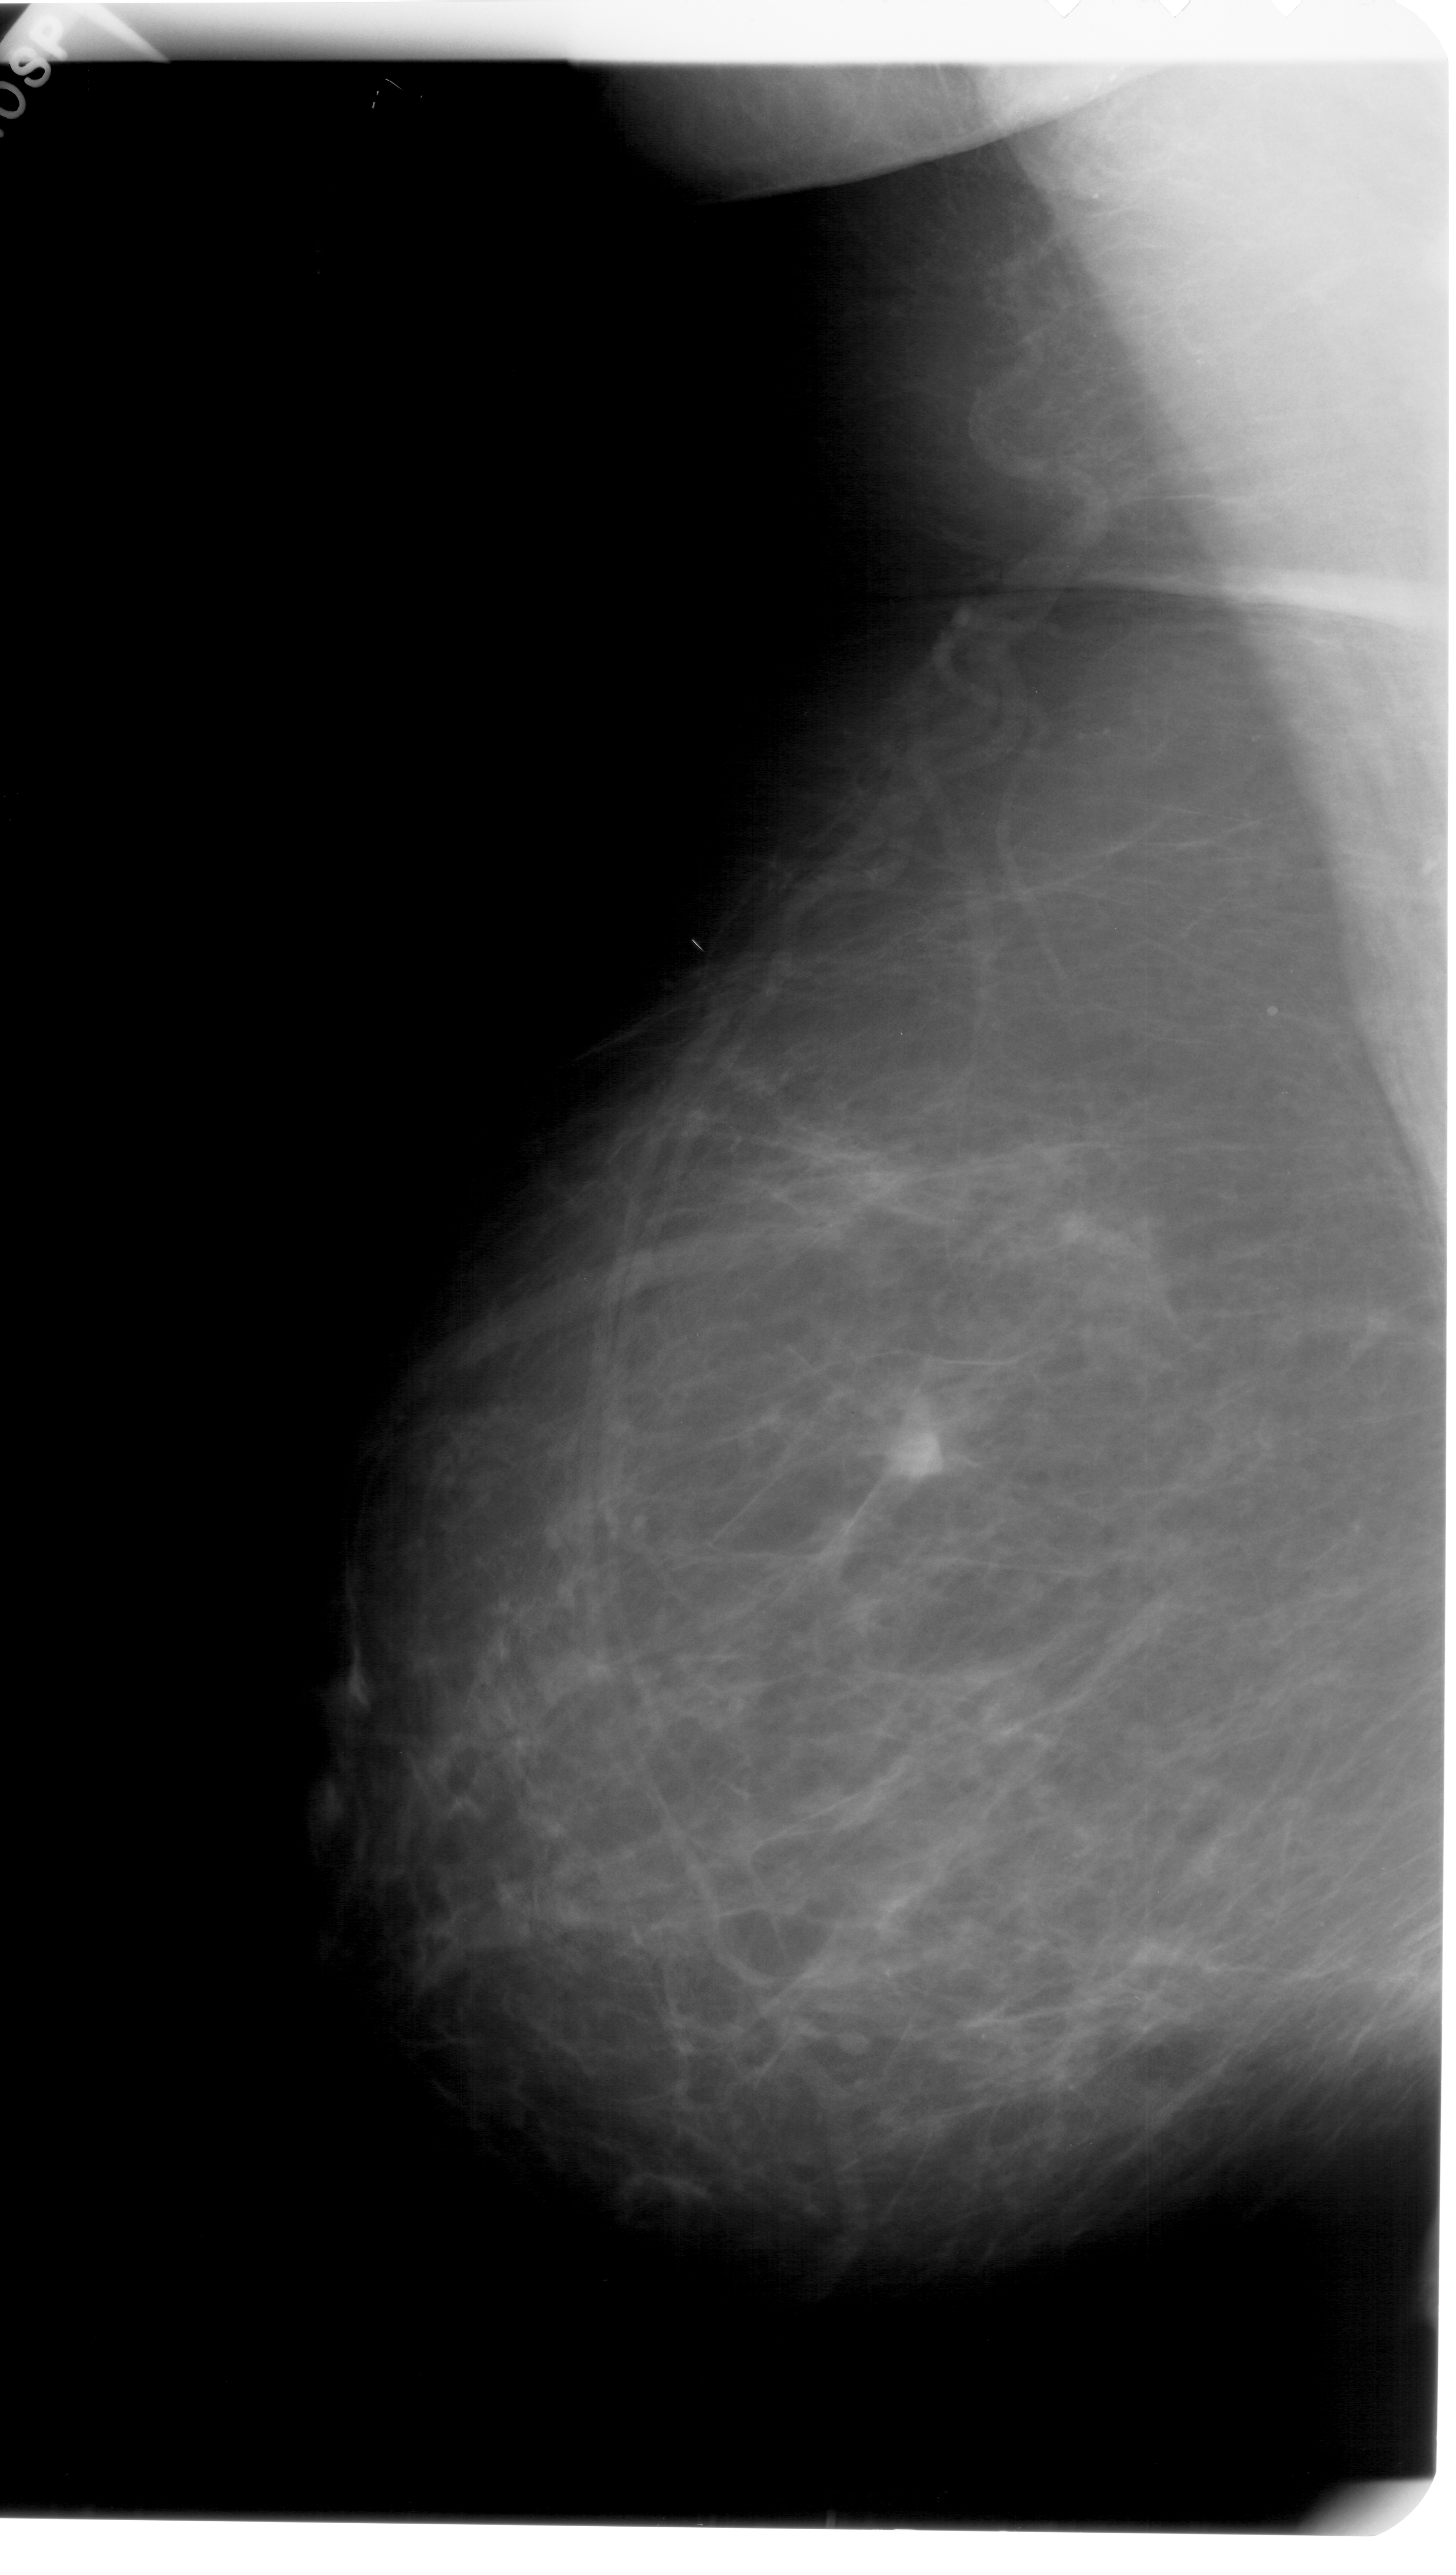
Digitized screen-film mammogram; left breast; MLO view; BI-RADS breast density category 2 (scale 1–4).
- Marked findings (only marked abnormalities are described; nothing is implied about the rest of the image): mass, shape irregular, margins ill defined; BI-RADS assessment category 4; subtlety rating 4 on a 1 (subtle) to 5 (obvious) scale; pathology result (as recorded, not read from the image): malignant.